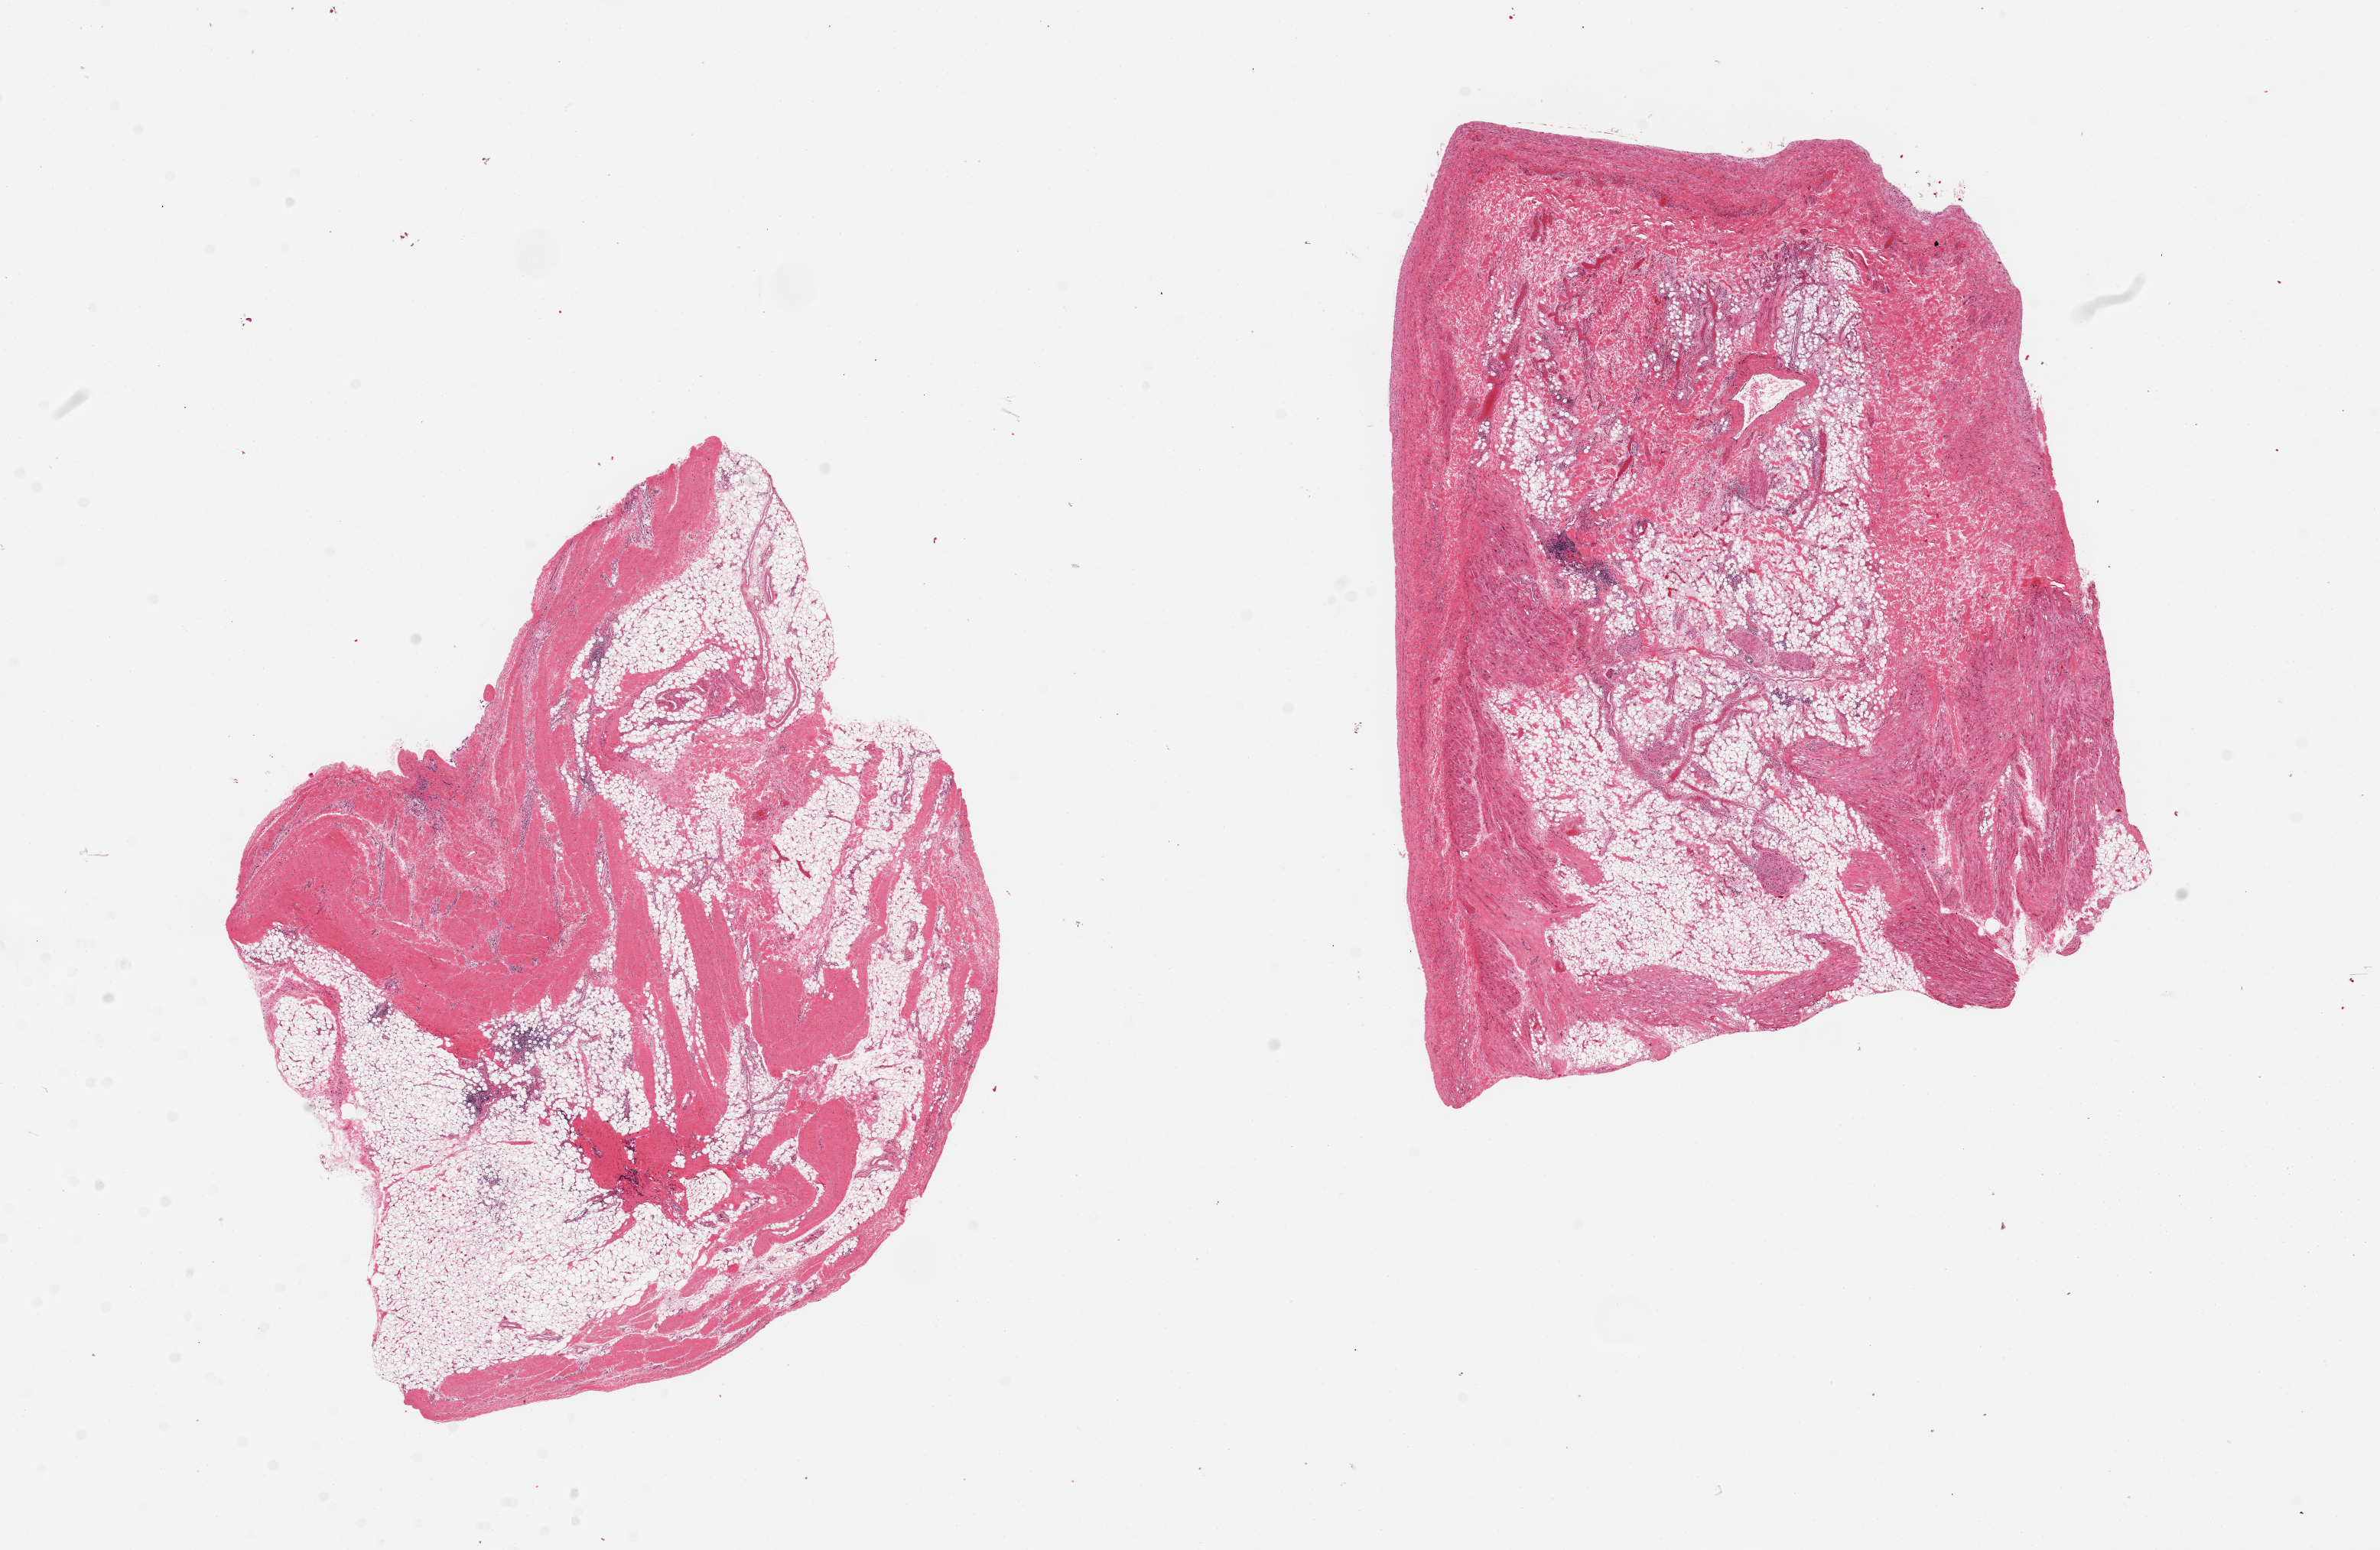
Digitized haematoxylin and eosin-stained section, brightfield — low-resolution overview of the scanned area, about 24.6 x 16.0 mm (acquisition: 20x scan); PAXgene-fixed paraffin-embedded (PFPE) section; target tissue: auricular appendage; tissue donor sample. Male donor.
Pathologist's review note for this sample: 2 pieces; both largely (80%) fibroadipose tissue; muscle is sparse and scattered; (history of atrial fibrillation).